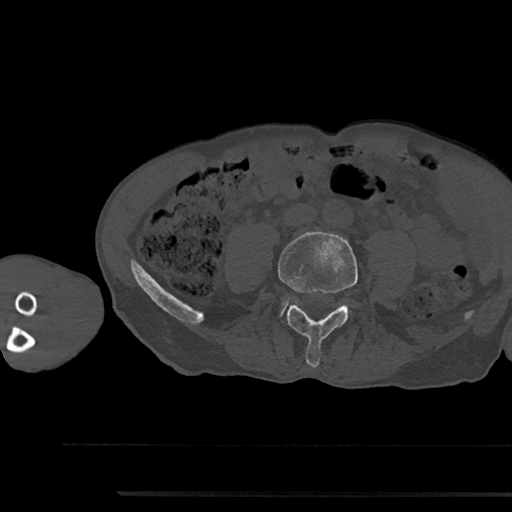
CT including the spine, one axial slice. Position 399 of 797 along the scan axis. 120 kVp. Bone window (W 1800 / L 400 HU). 0.5 mm slice thickness. 512 × 512 image matrix, field of view 367 × 367 mm. Male patient, age 79 years. From the clinical record (not read from this slice): primary cancer: prostate.
Structures marked on this image (semi-automatically segmented with operator editing):
- L4 vertebra: bounding box <278,231,358,367> (left, top, right, bottom; pixels)
- L5 vertebra: <281,309,284,313>